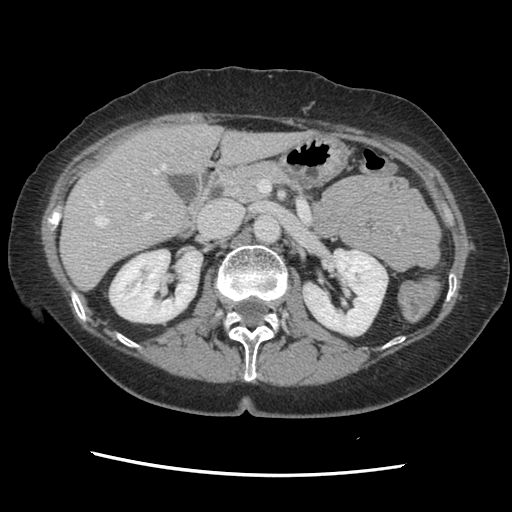
Contrast-enhanced abdominal CT, one axial slice. Soft-tissue window (W 400 / L 40 HU). 512 × 512 image matrix, field of view 330 × 330 mm. Female patient, age 61 years. Case-level facts recorded for this patient, not image findings: diagnosis: colorectal cancer liver metastases, imaged before liver resection; multiple liver metastases: no; largest metastasis: 2.4 cm.
Outlined on this slice (expert manual segmentation):
- hepatic veins: bounding box (x1, y1, x2, y2) in pixels: (85, 148, 173, 268)
- liver: (62, 125, 301, 289)
- planned liver remnant (the part of the liver to remain after resection): (62, 125, 301, 289)
- portal vein (with intrahepatic branches): (92, 184, 152, 245)